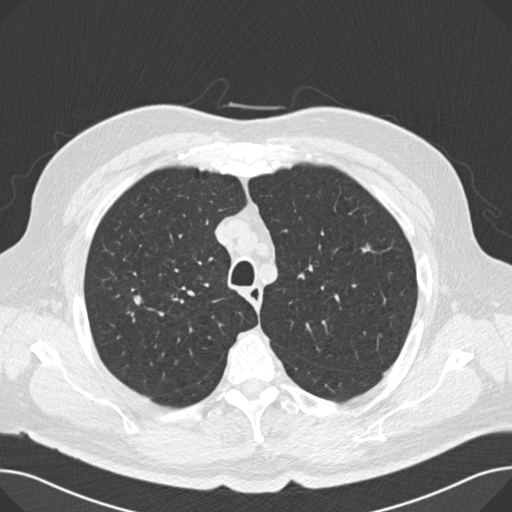
Axial slice from a low-dose chest CT screening exam; second annual screen; lung window (W 1500 / L -600 HU); 2 mm slice thickness; slice 39 of 166 in the series; 512 × 512 image matrix. Male participant, aged 67 years at enrolment. Current smoker at enrolment.
Lesion marked by an expert reader, bounding box [x1, y1, x2, y2] px = [127, 289, 147, 310]. No non-calcified nodule or mass ≥4 mm was recorded by the screening reader at this exam. Participant outcome: lung cancer diagnosed 194 days after this screen — small cell carcinoma, NOS, right middle lobe, stage IA (AJCC 6th edition), 20 mm at pathology.